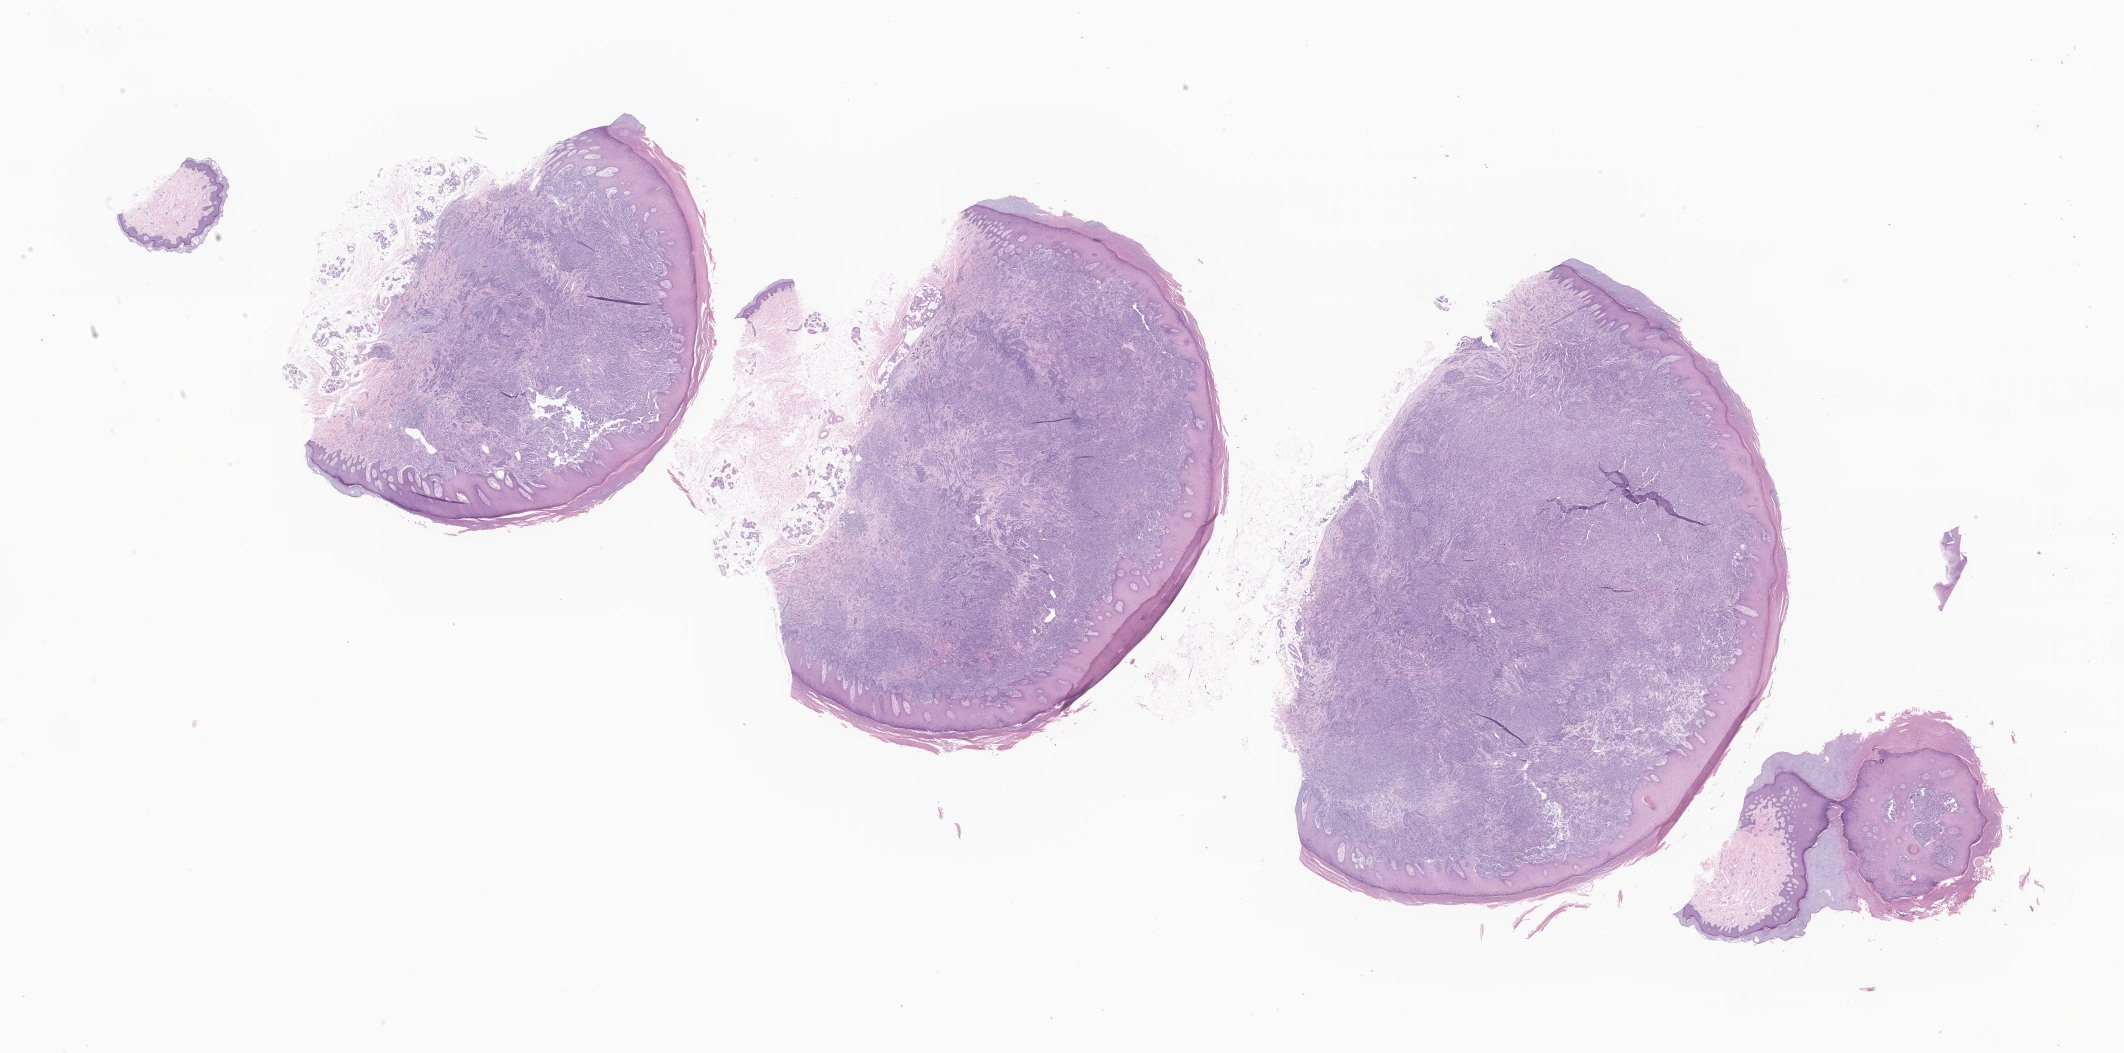
Digitized haematoxylin and eosin-stained section of tumor tissue from the soft tissue — whole scanned area (about 35.8 x 17.8 mm) shown as a low-resolution overview; formalin-fixed paraffin-embedded section. Patient female; age 247 months.
Diagnosis (ICD-O-3 morphology term): Clear cell sarcoma, NOS.